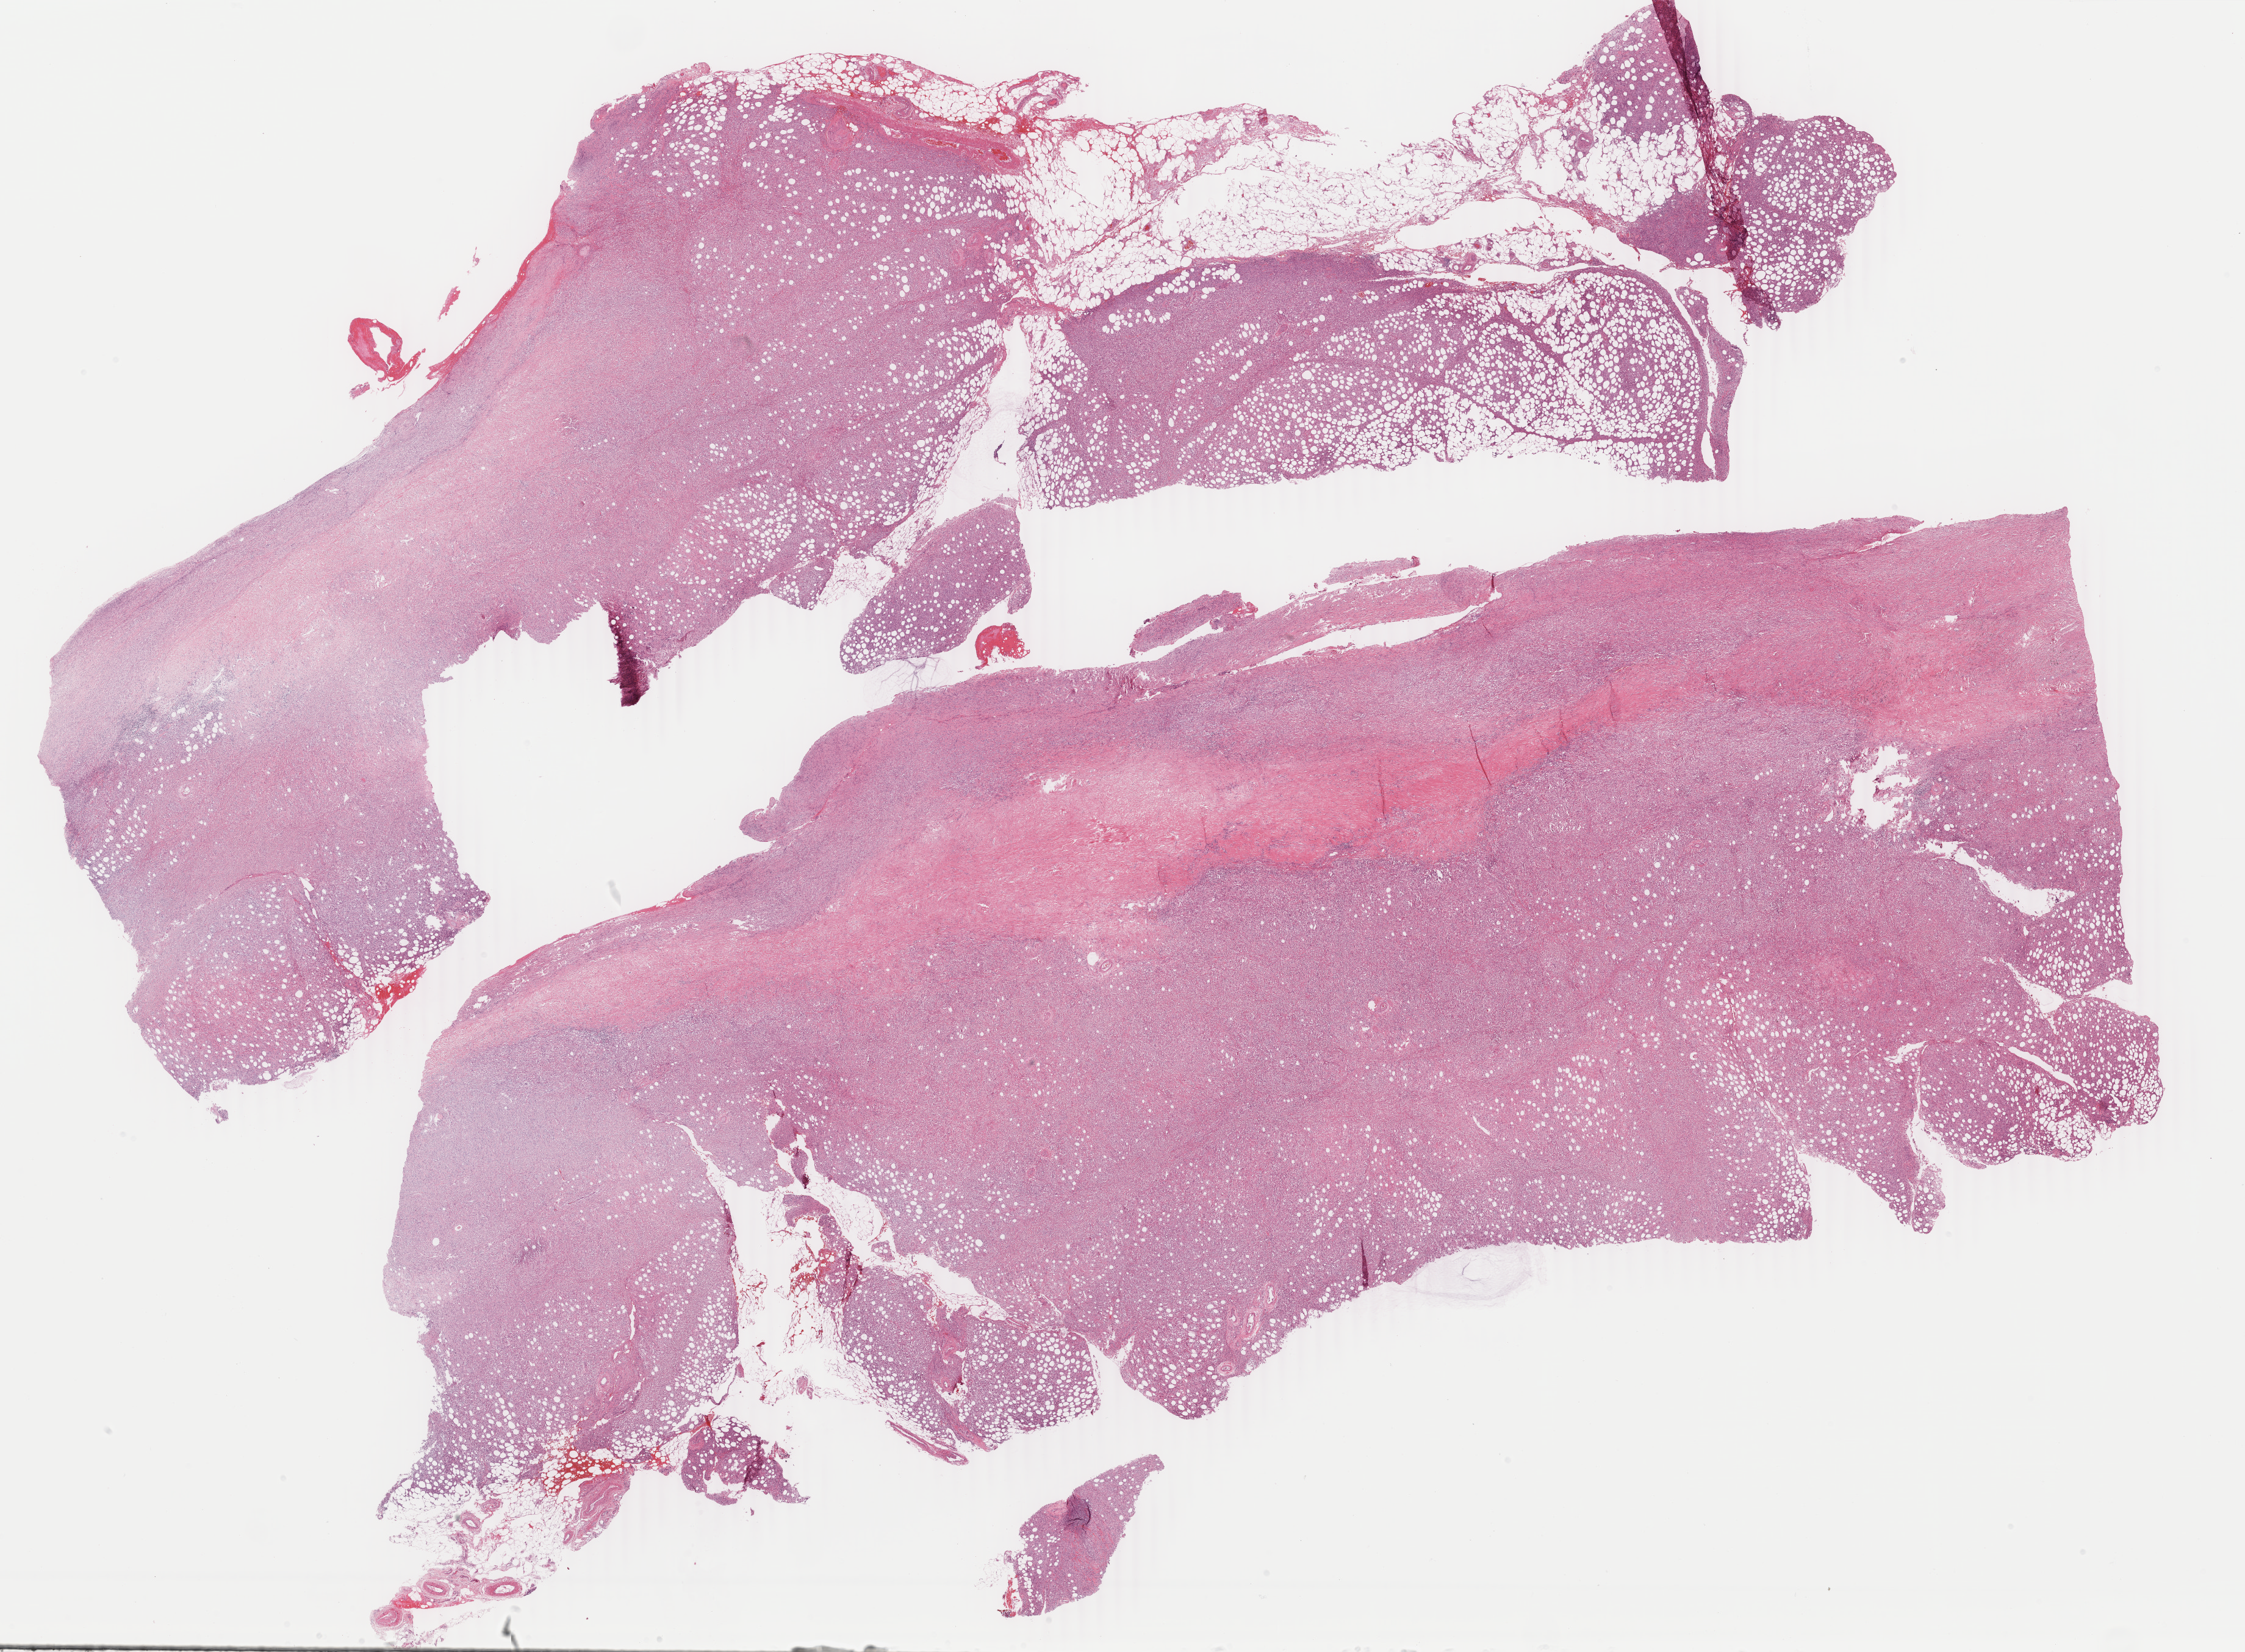
Whole-slide histology image, H&E — low-resolution overview of the scanned area, about 29.3 x 21.5 mm, formalin-fixed paraffin-embedded (FFPE) diagnostic section, primary tumour sample from the mesothelium. Male, age 81 years at initial diagnosis.
Laterality: left. Diagnosis: Mesothelioma, malignant (pleura, NOS). AJCC pathologic stage: IA (6th edition).